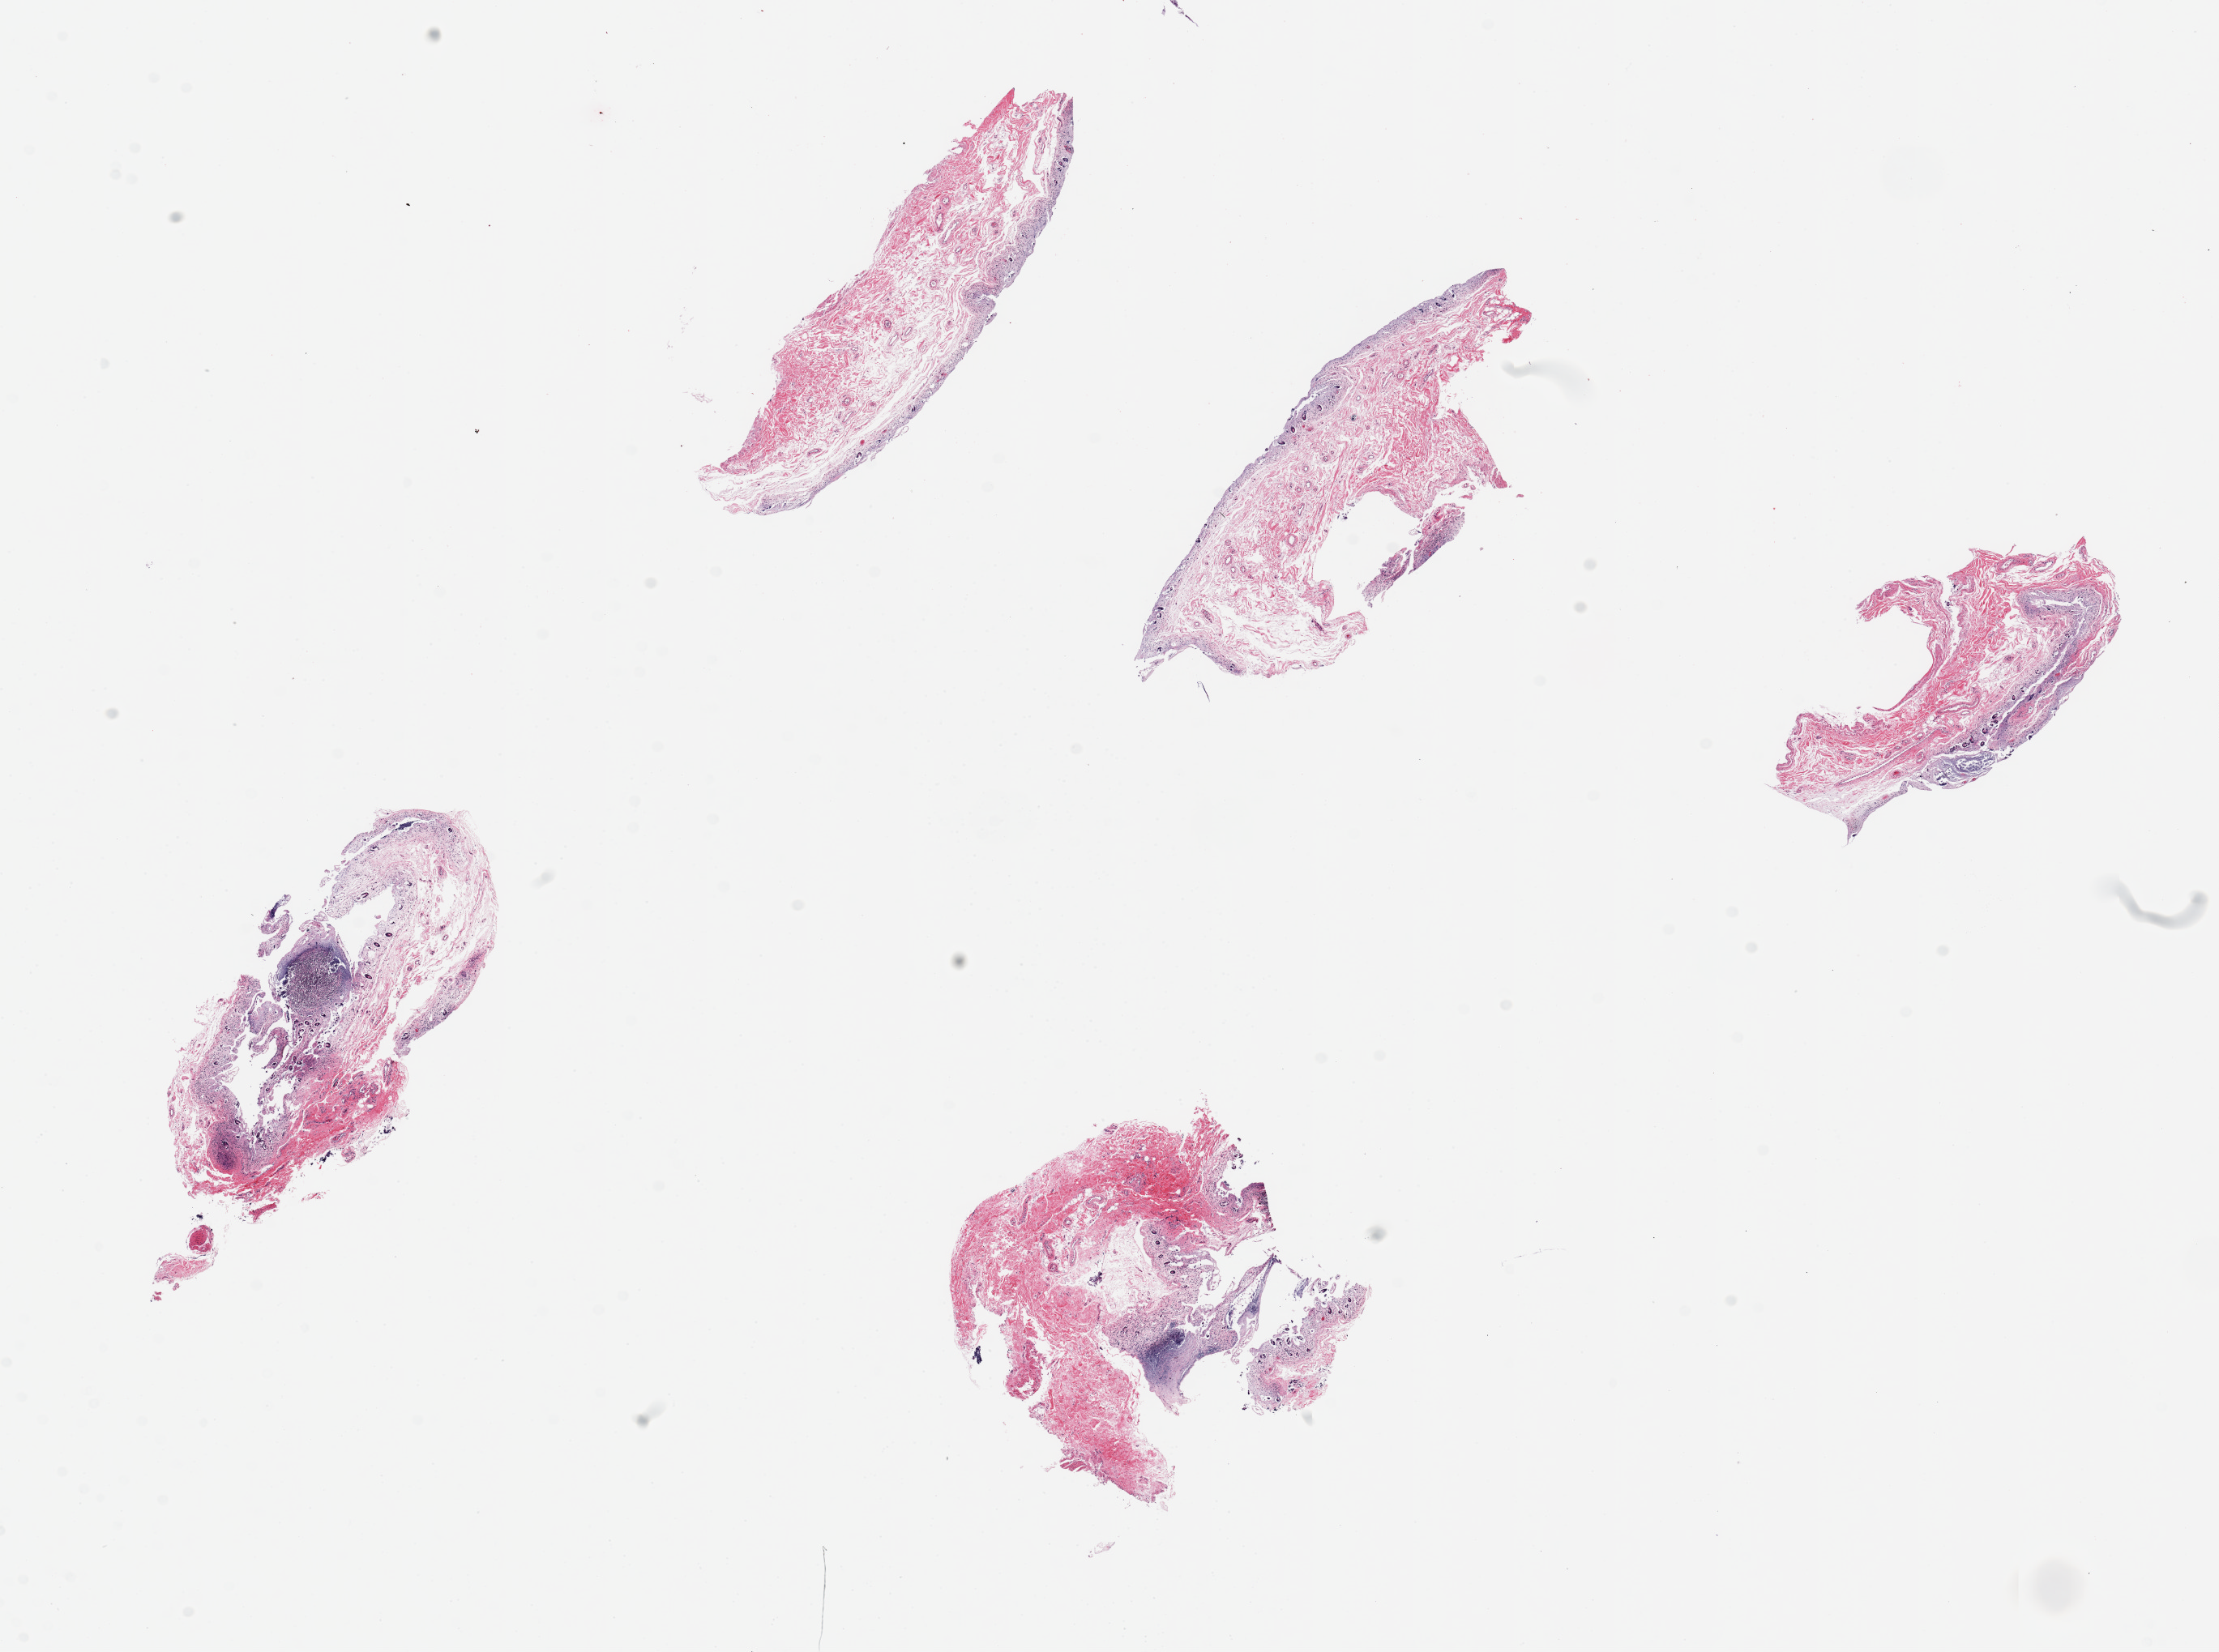
Digitized hematoxylin and eosin (H&E)-stained section — whole scanned area (about 21.7 x 16.1 mm, acquisition: 20x scan) shown as a low-resolution overview; PAXgene-fixed, paraffin-embedded tissue; sampled site (target tissue): ileum; tissue donor sample. Donor: male.
Review note (as recorded): 5 pieces ~5x.15mm. Badly autolyzed.